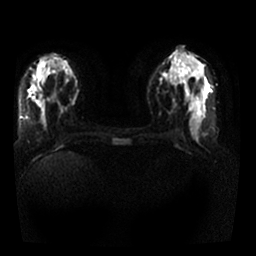
Breast MRI, one axial slice. Slice 11 of 25 in the series (ordered by position). Diffusion-weighted series; image 2 of 4 stored at this slice position (different b-values; order by instance number). 1.5 T. 4 mm slice thickness. 256 × 256 image matrix. Female patient.
Structures marked on this image (manually delineated by an expert):
- tumour on diffusion-weighted imaging: bounding box <31,87,42,106> (left, top, right, bottom; pixels)